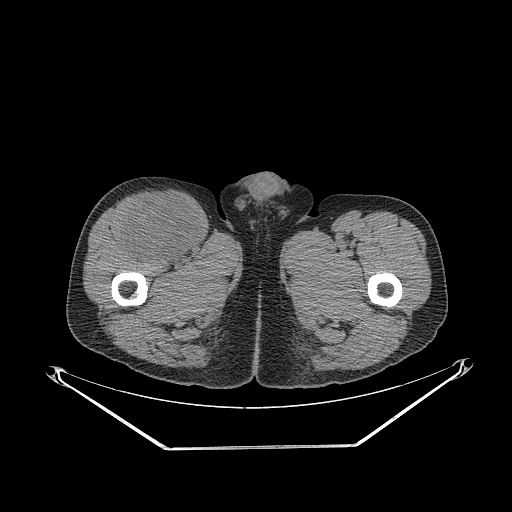
CT of an extremity soft-tissue mass (from a PET/CT study), one axial slice; slice 296 of 311 in the series (ordered by position); reconstruction kernel STANDARD; 140 kVp; soft-tissue window (W 400 / L 40 HU); 3.75 mm slice thickness; 512 × 512 image matrix, field of view 500 × 500 mm. Male patient. From the clinical record (not read from this slice): histological type: pleiomorphic leiomyosarcoma; grade: intermediate; site of the primary tumour: right thigh.
Outlined on this slice (expert contour drawn on MRI and transferred to this co-registered scan by the dataset authors):
- gross tumour volume including surrounding oedema: box from (x=121, y=194) to (x=202, y=263) px
- gross tumour volume (mass): (x=123, y=194)–(x=202, y=263)